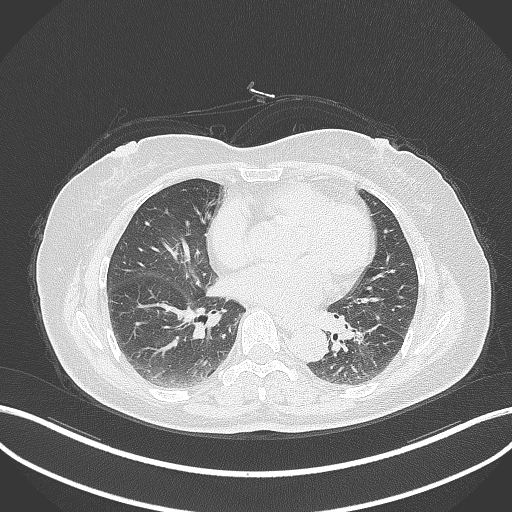
Chest CT, one axial slice. Position 168 of 311 along the scan axis. Lung window (W 1500 / L -600 HU). 1 mm slice thickness. 512 × 512 image matrix, field of view 400 × 400 mm. Female patient, age 59 years. Case-level facts recorded for this patient, not image findings: clinical TNM (as recorded): T2a N0 M0.
Structures marked on this image (bounding box drawn by a radiologist):
- lung tumour (recorded histology: adenocarcinoma): box from (x=353, y=319) to (x=382, y=348) px